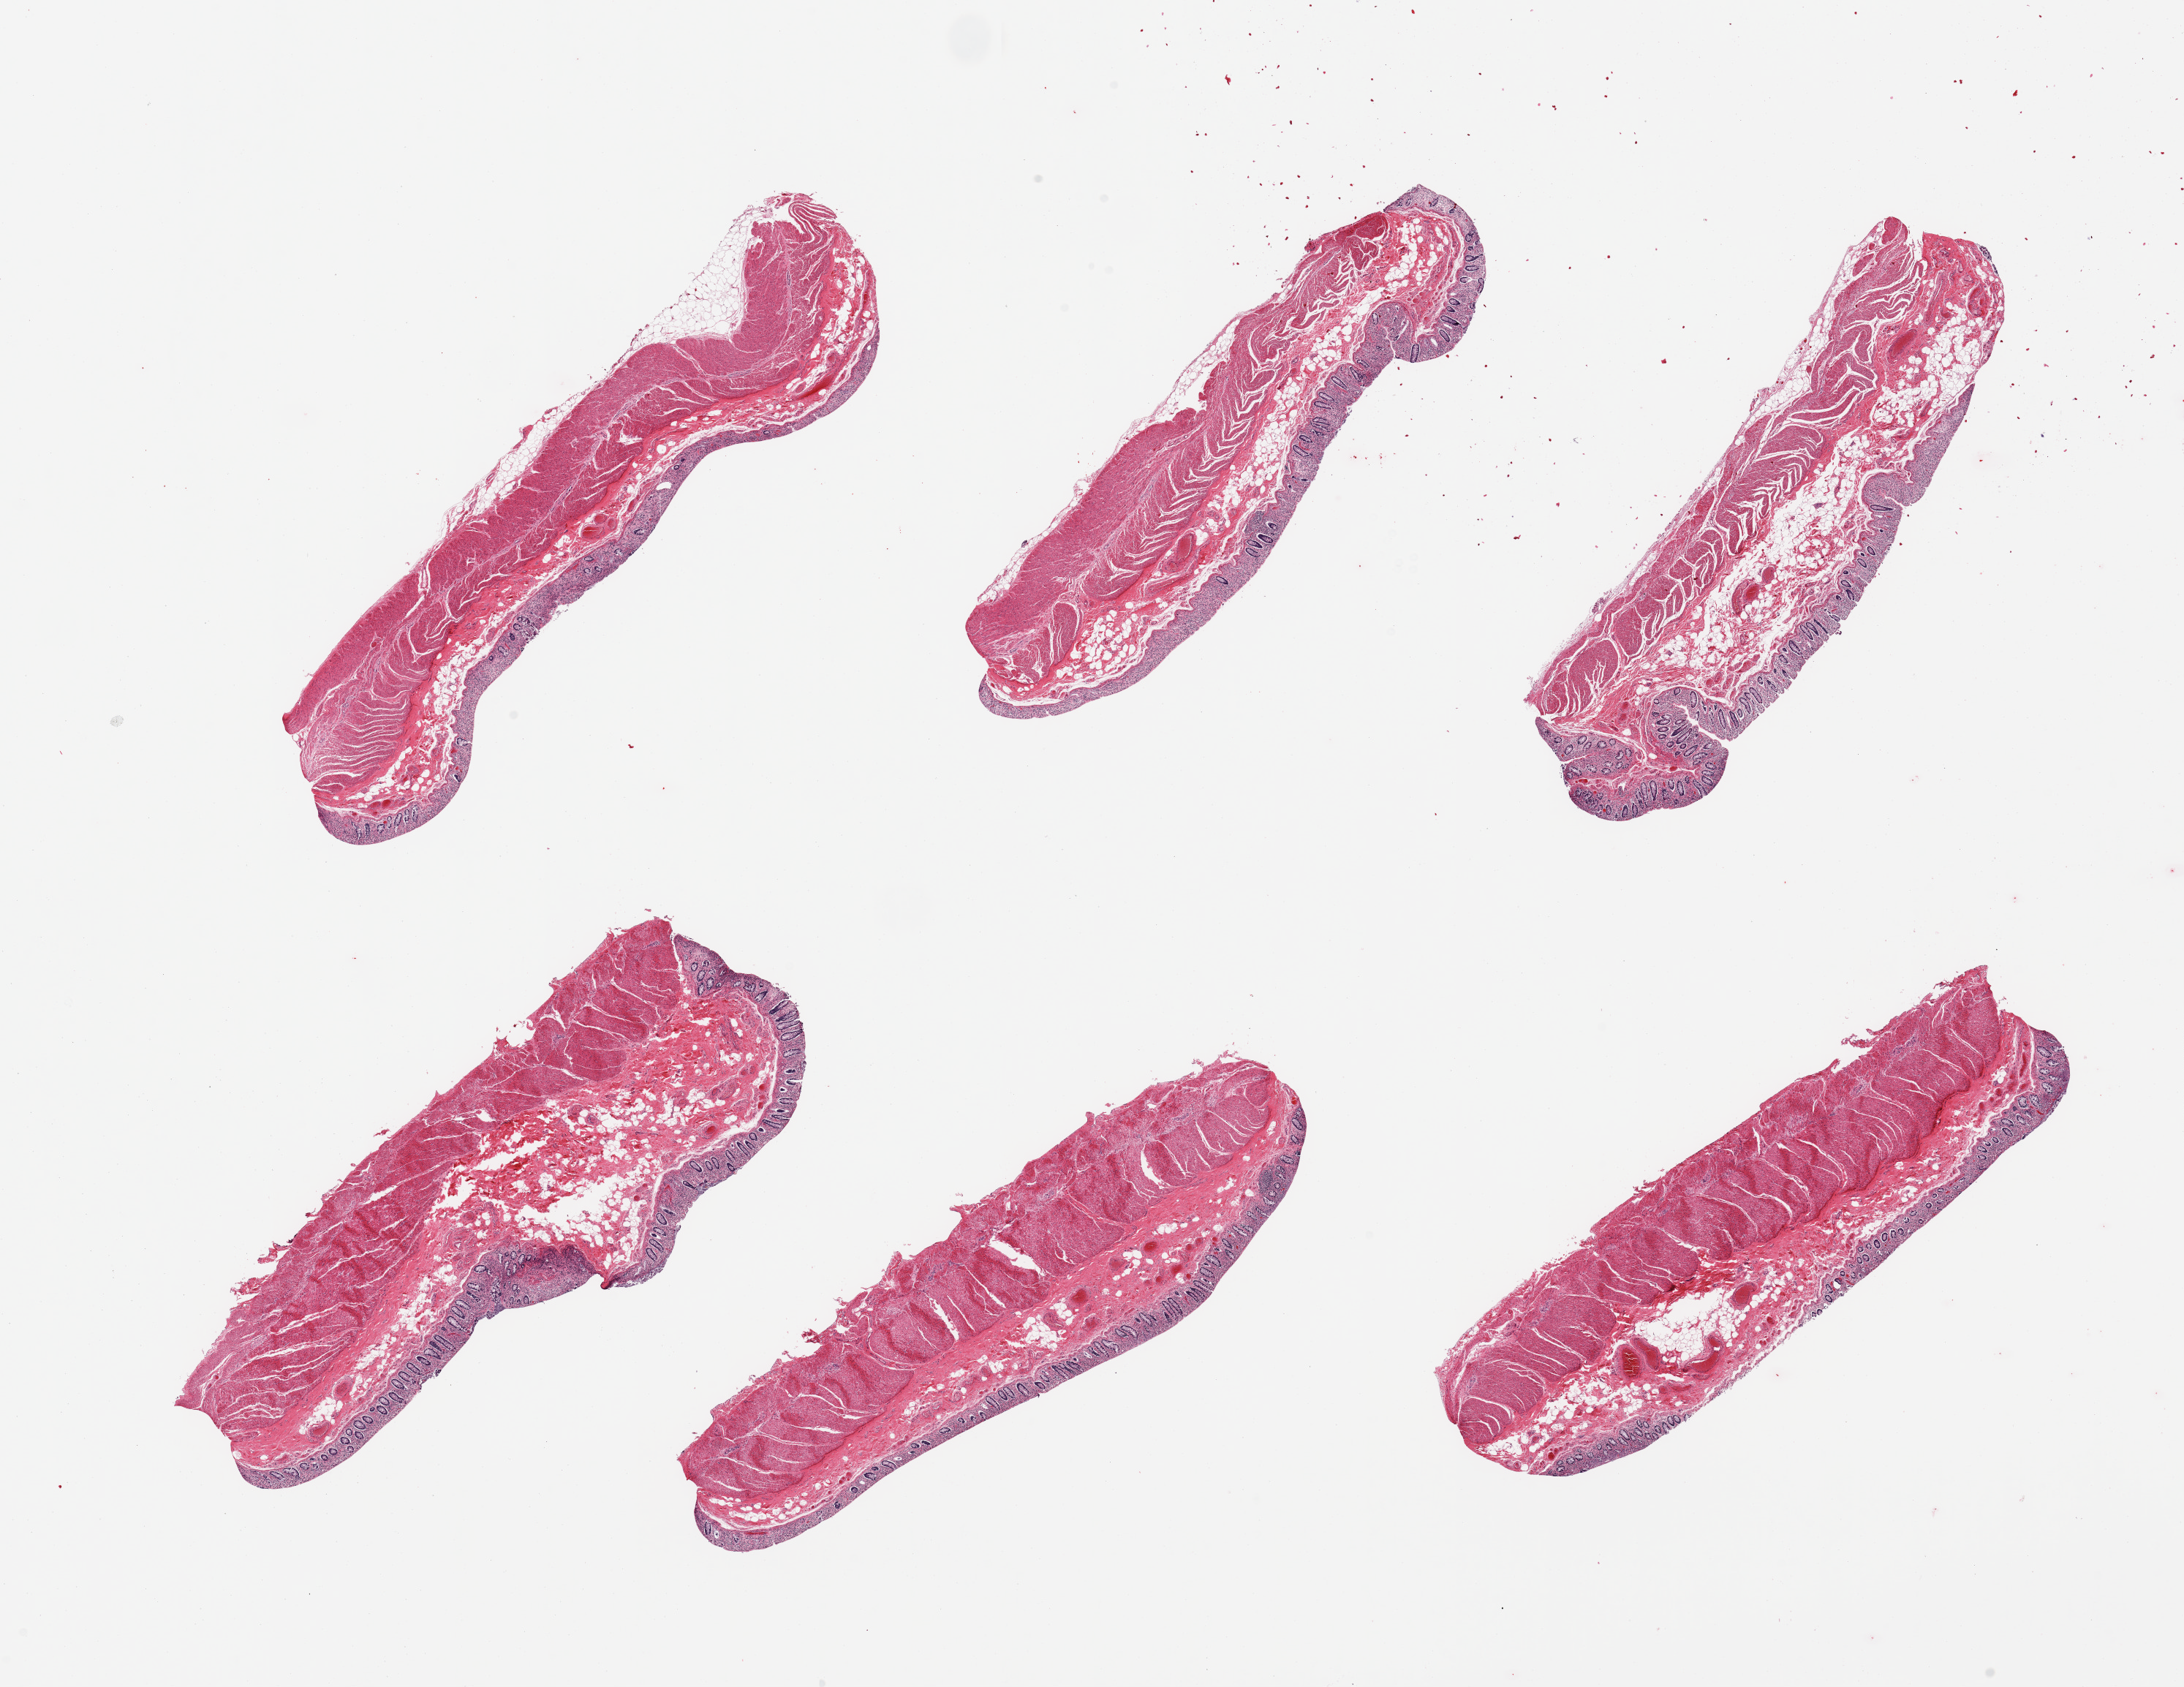
Whole-slide image, H&E stain, brightfield, a low-resolution overview of the entire scanned area, about 23.6 x 18.2 mm; PAXgene-fixed paraffin-embedded (PFPE) section; sampled site (target tissue): transverse colon; tissue donor sample. Donor sex: female.
- review note (as recorded): 6 pieces; autolyzed mucosa, muscle intact